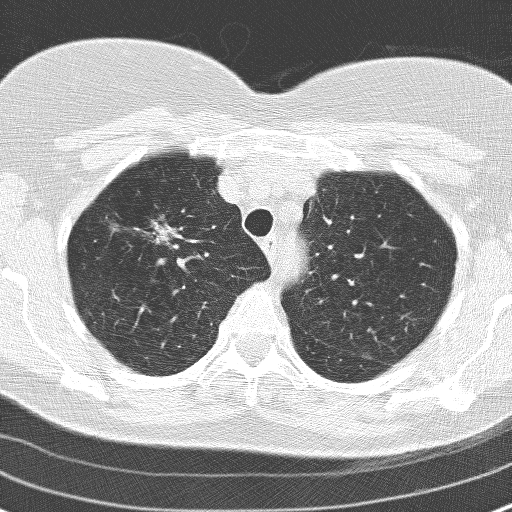
Axial slice from a low-dose chest CT screening exam; second annual screen; lung window (W 1500 / L -600 HU); 3.2 mm slice thickness; 120 kVp; slice 36 of 160 in the series; 512 × 512 image matrix. Female participant, aged 60 years at enrolment. Former smoker at enrolment.
- Expert-annotated lung lesion, box from (x=124, y=209) to (x=179, y=257) px.
- Screening reader's record for this exam (one nodule recorded; not confirmed to be the boxed lesion): non-calcified nodule or mass ≥4 mm, right upper lobe, 17 × 15 mm, spiculated (stellate) margins, soft tissue attenuation, pre-existing on the prior screen: yes; interval growth: yes.